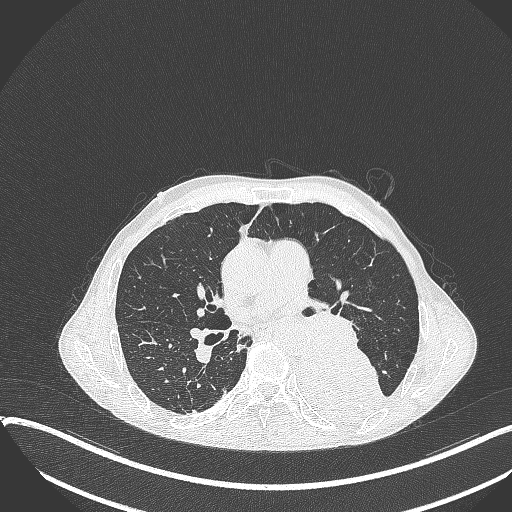
Chest CT, one axial slice. Reconstruction kernel B70f. Lung window (W 1500 / L -600 HU). 1 mm slice thickness. 512 × 512 image matrix. Patient: male, 57 years. Case-level facts recorded for this patient, not image findings: clinical TNM (as recorded): T4 N0 M0.
Structures marked on this image (rectangle marked by the reading radiologist):
- lung tumour (recorded histology: squamous cell carcinoma): bounding box (x1, y1, x2, y2) in pixels: (292, 343, 384, 422)